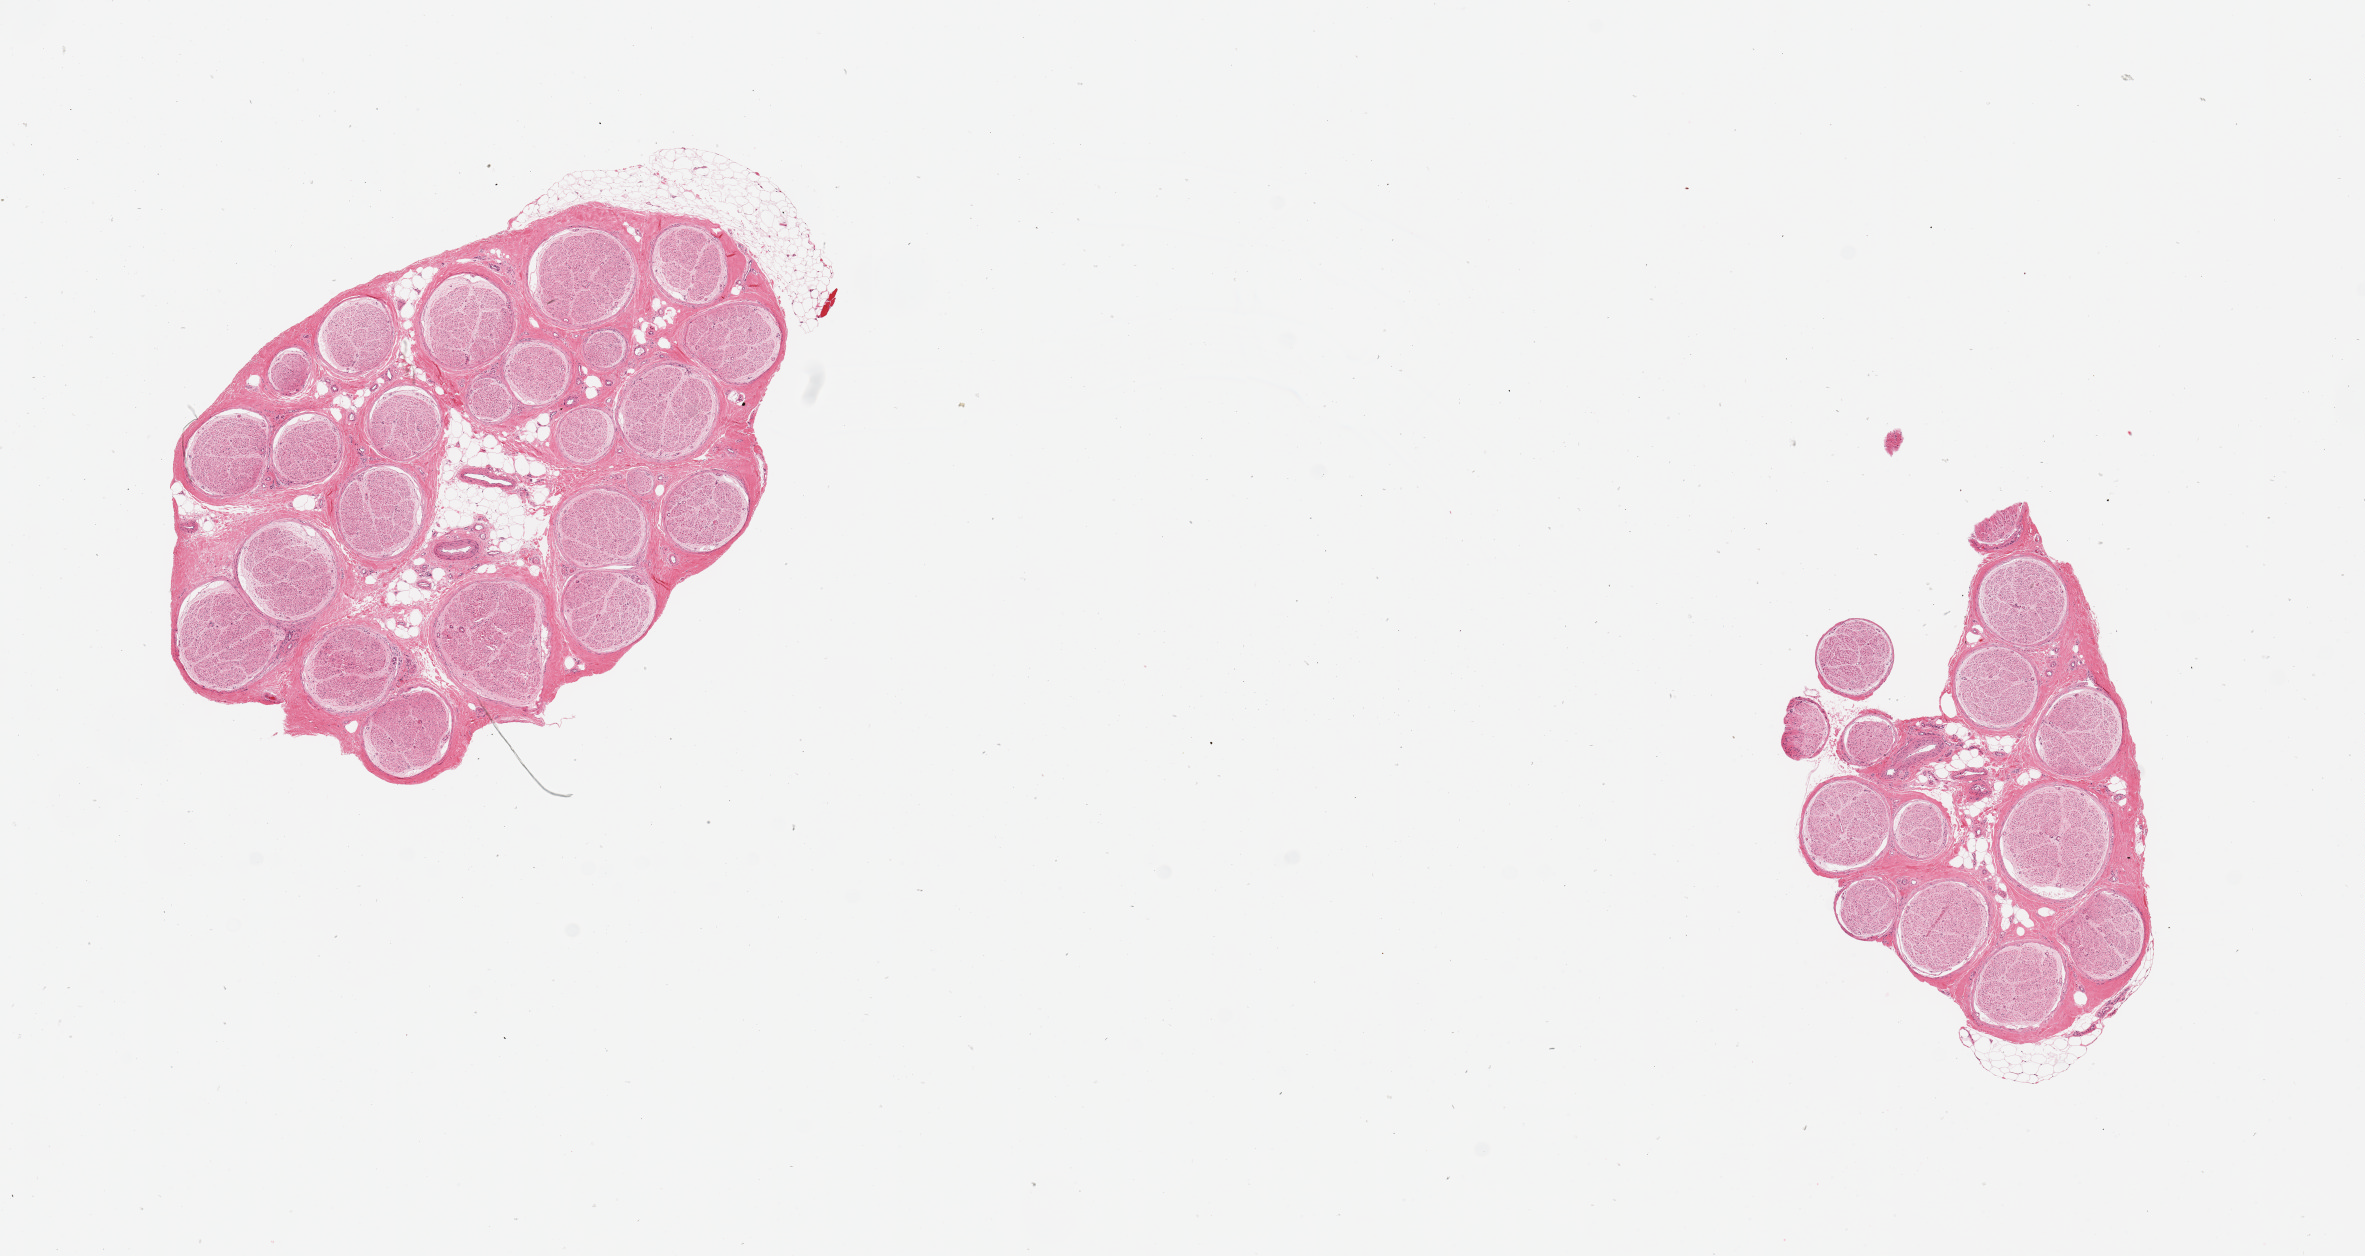
Whole-slide image, hematoxylin and eosin (H&E) stain, brightfield, shown as a low-resolution overview of the whole scanned area (about 18.7 x 9.9 mm). PAXgene-fixed paraffin-embedded (PFPE) section. Target tissue: tibial nerve. Tissue donor sample. Donor: male.
* pathologist's review note for this sample: 2 pieces, up to 10% attached and internal fat